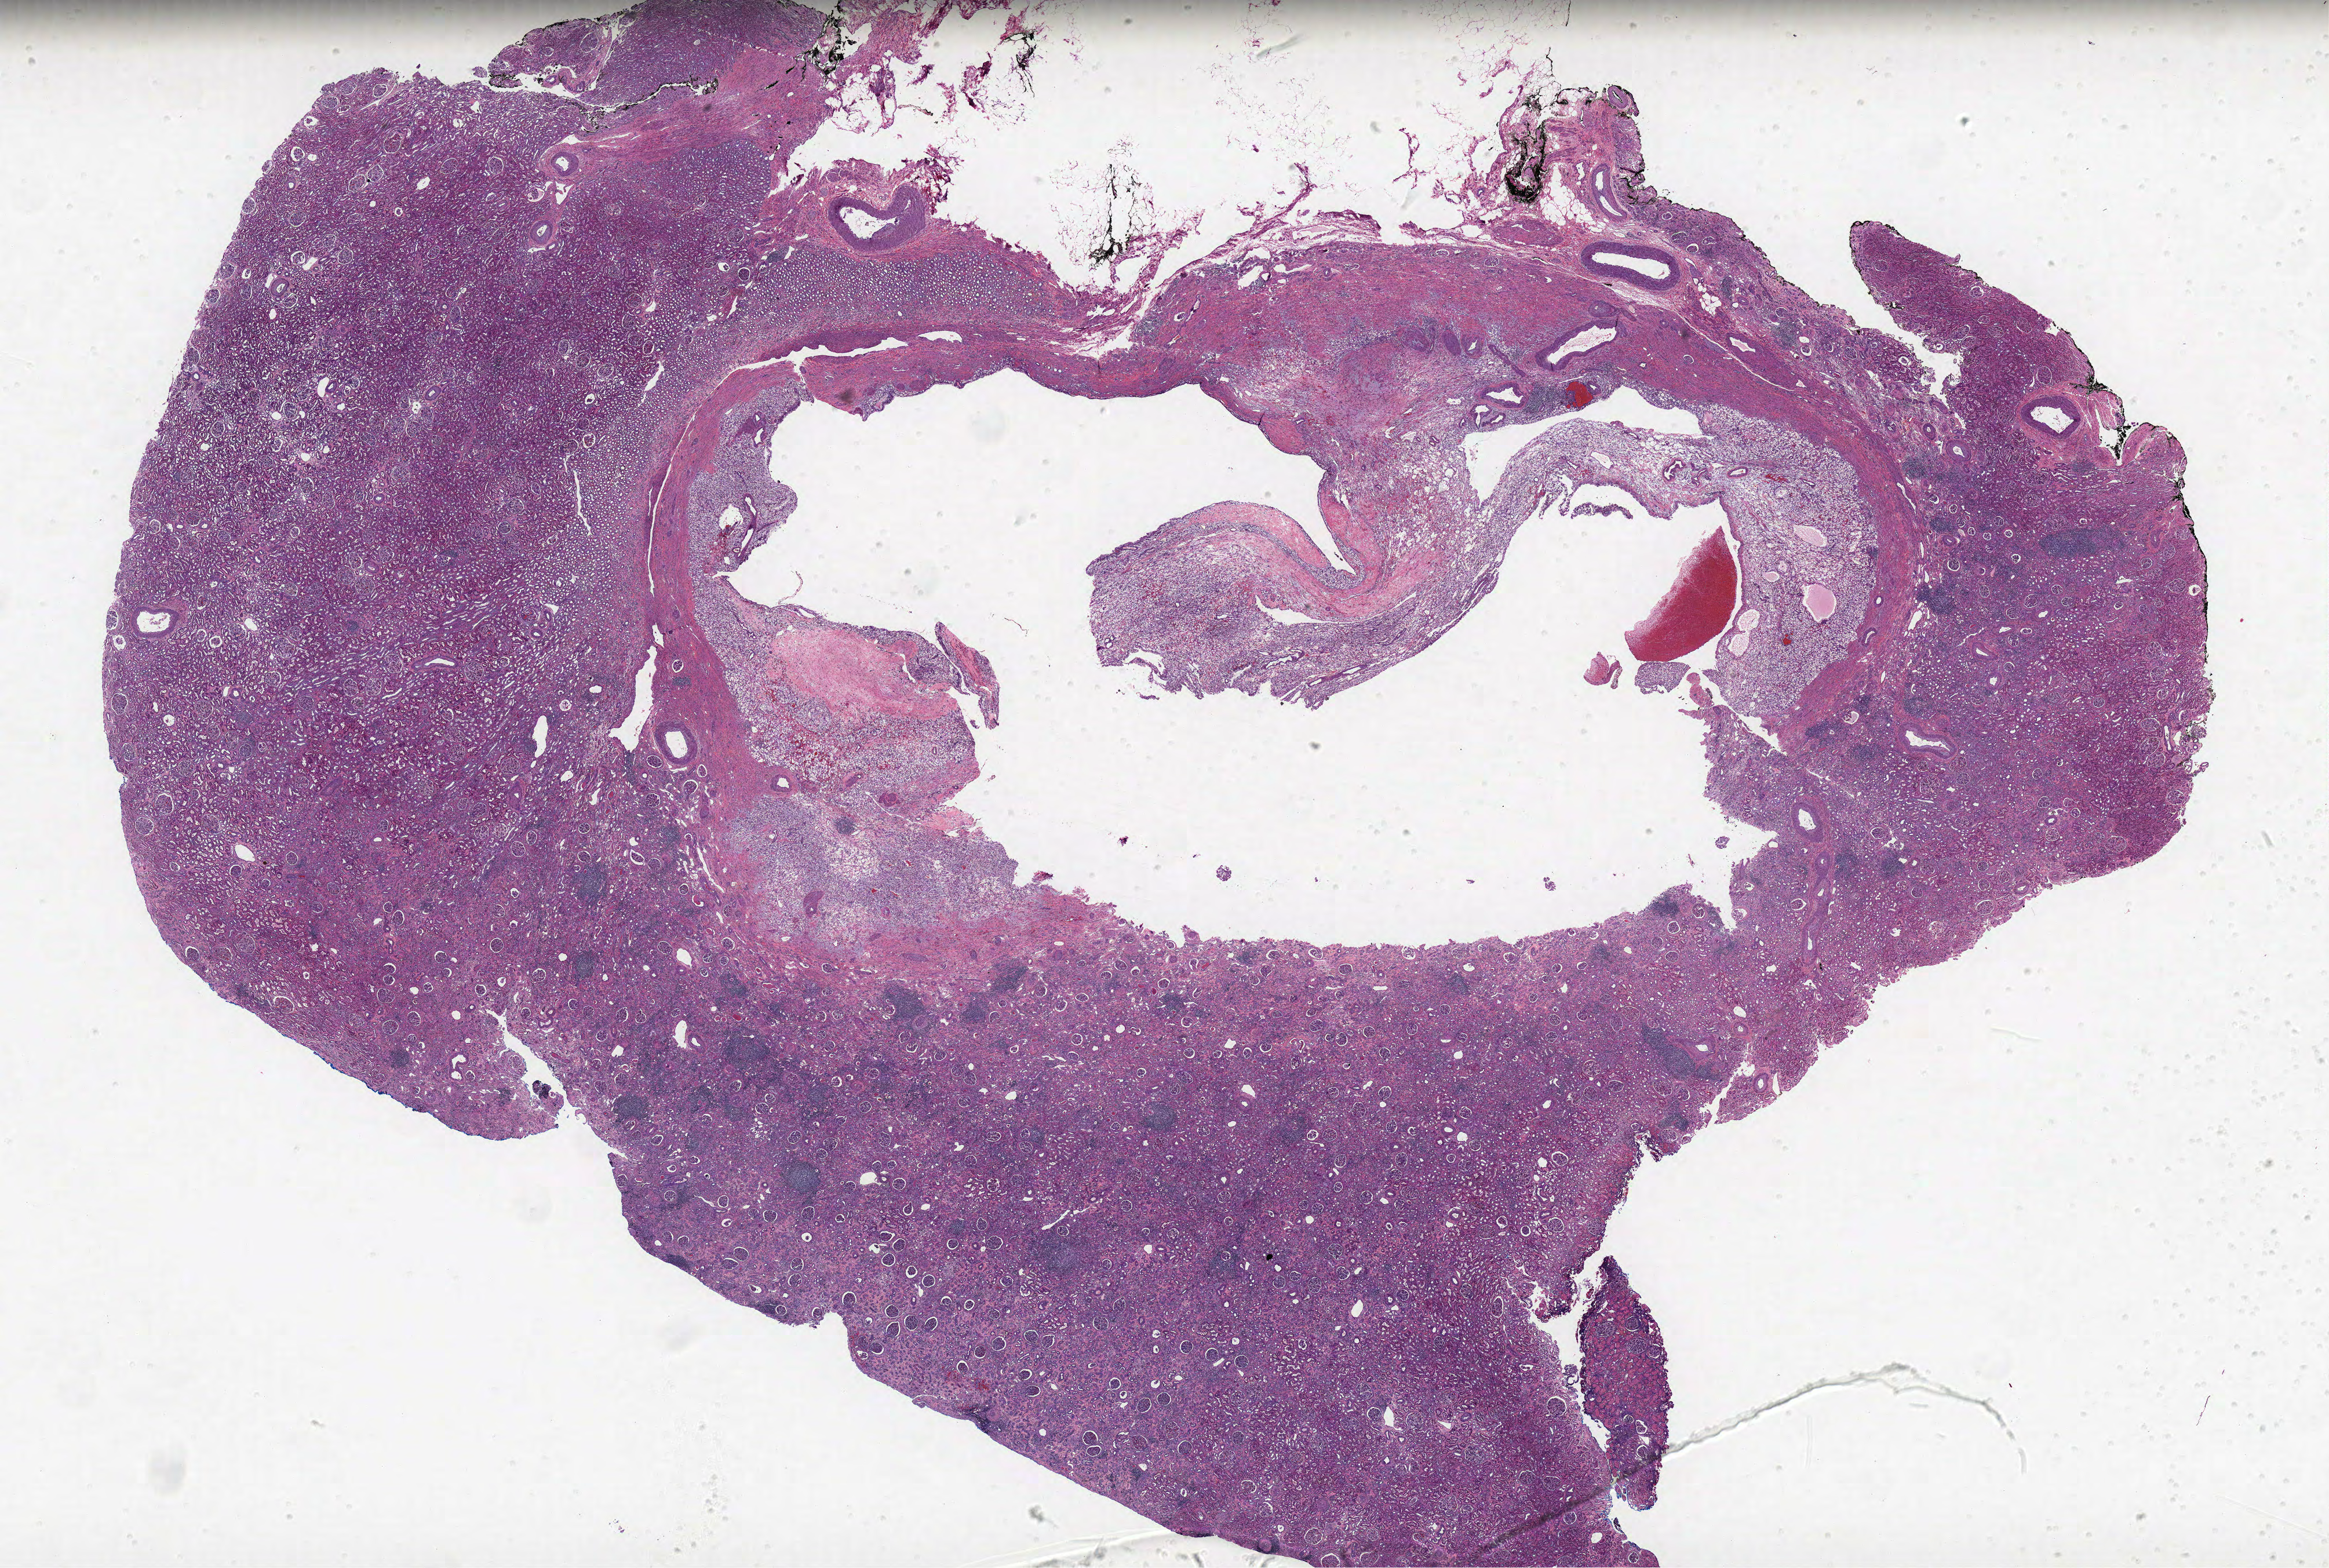
H&E-stained whole-slide image — low-resolution overview of the scanned area, about 32.1 x 21.6 mm (from a 40x scan); formalin-fixed paraffin-embedded (FFPE) diagnostic section; sample: primary tumour, kidney. Patient: male, age at initial diagnosis 46 years. Histologic grade: G2 (moderately differentiated).
Laterality: left. Histologic diagnosis: Clear cell adenocarcinoma, NOS. AJCC pathologic stage: I.